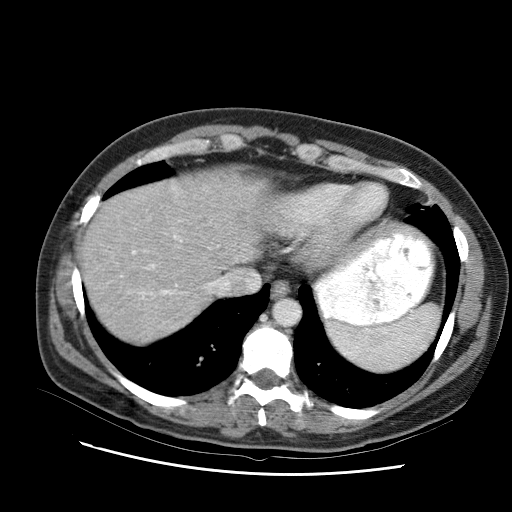
Contrast-enhanced abdominal CT (liver protocol), one axial slice. Position 81 of 95 along the scan axis. One of 2 acquisitions stored at this slice position. Soft-tissue window (W 400 / L 40 HU). 512 × 512 image matrix, field of view 360 × 360 mm. Case-level facts recorded for this patient, not image findings: diagnosis: hepatocellular carcinoma (patient treated with transarterial chemoembolisation; whether this scan precedes or follows treatment is not stated here); TNM stage (as recorded): Stage-I; Child-Pugh class: B; tumour nodularity: uninodular.
Structures marked on this image (semi-automatically segmented with operator editing):
- liver parenchyma outside the tumour (the mass and vessels are separate outlines, so this box may not span the whole liver): bounding box (x1, y1, x2, y2) in pixels: (84, 184, 261, 318)
- liver vessels: (119, 237, 145, 291)